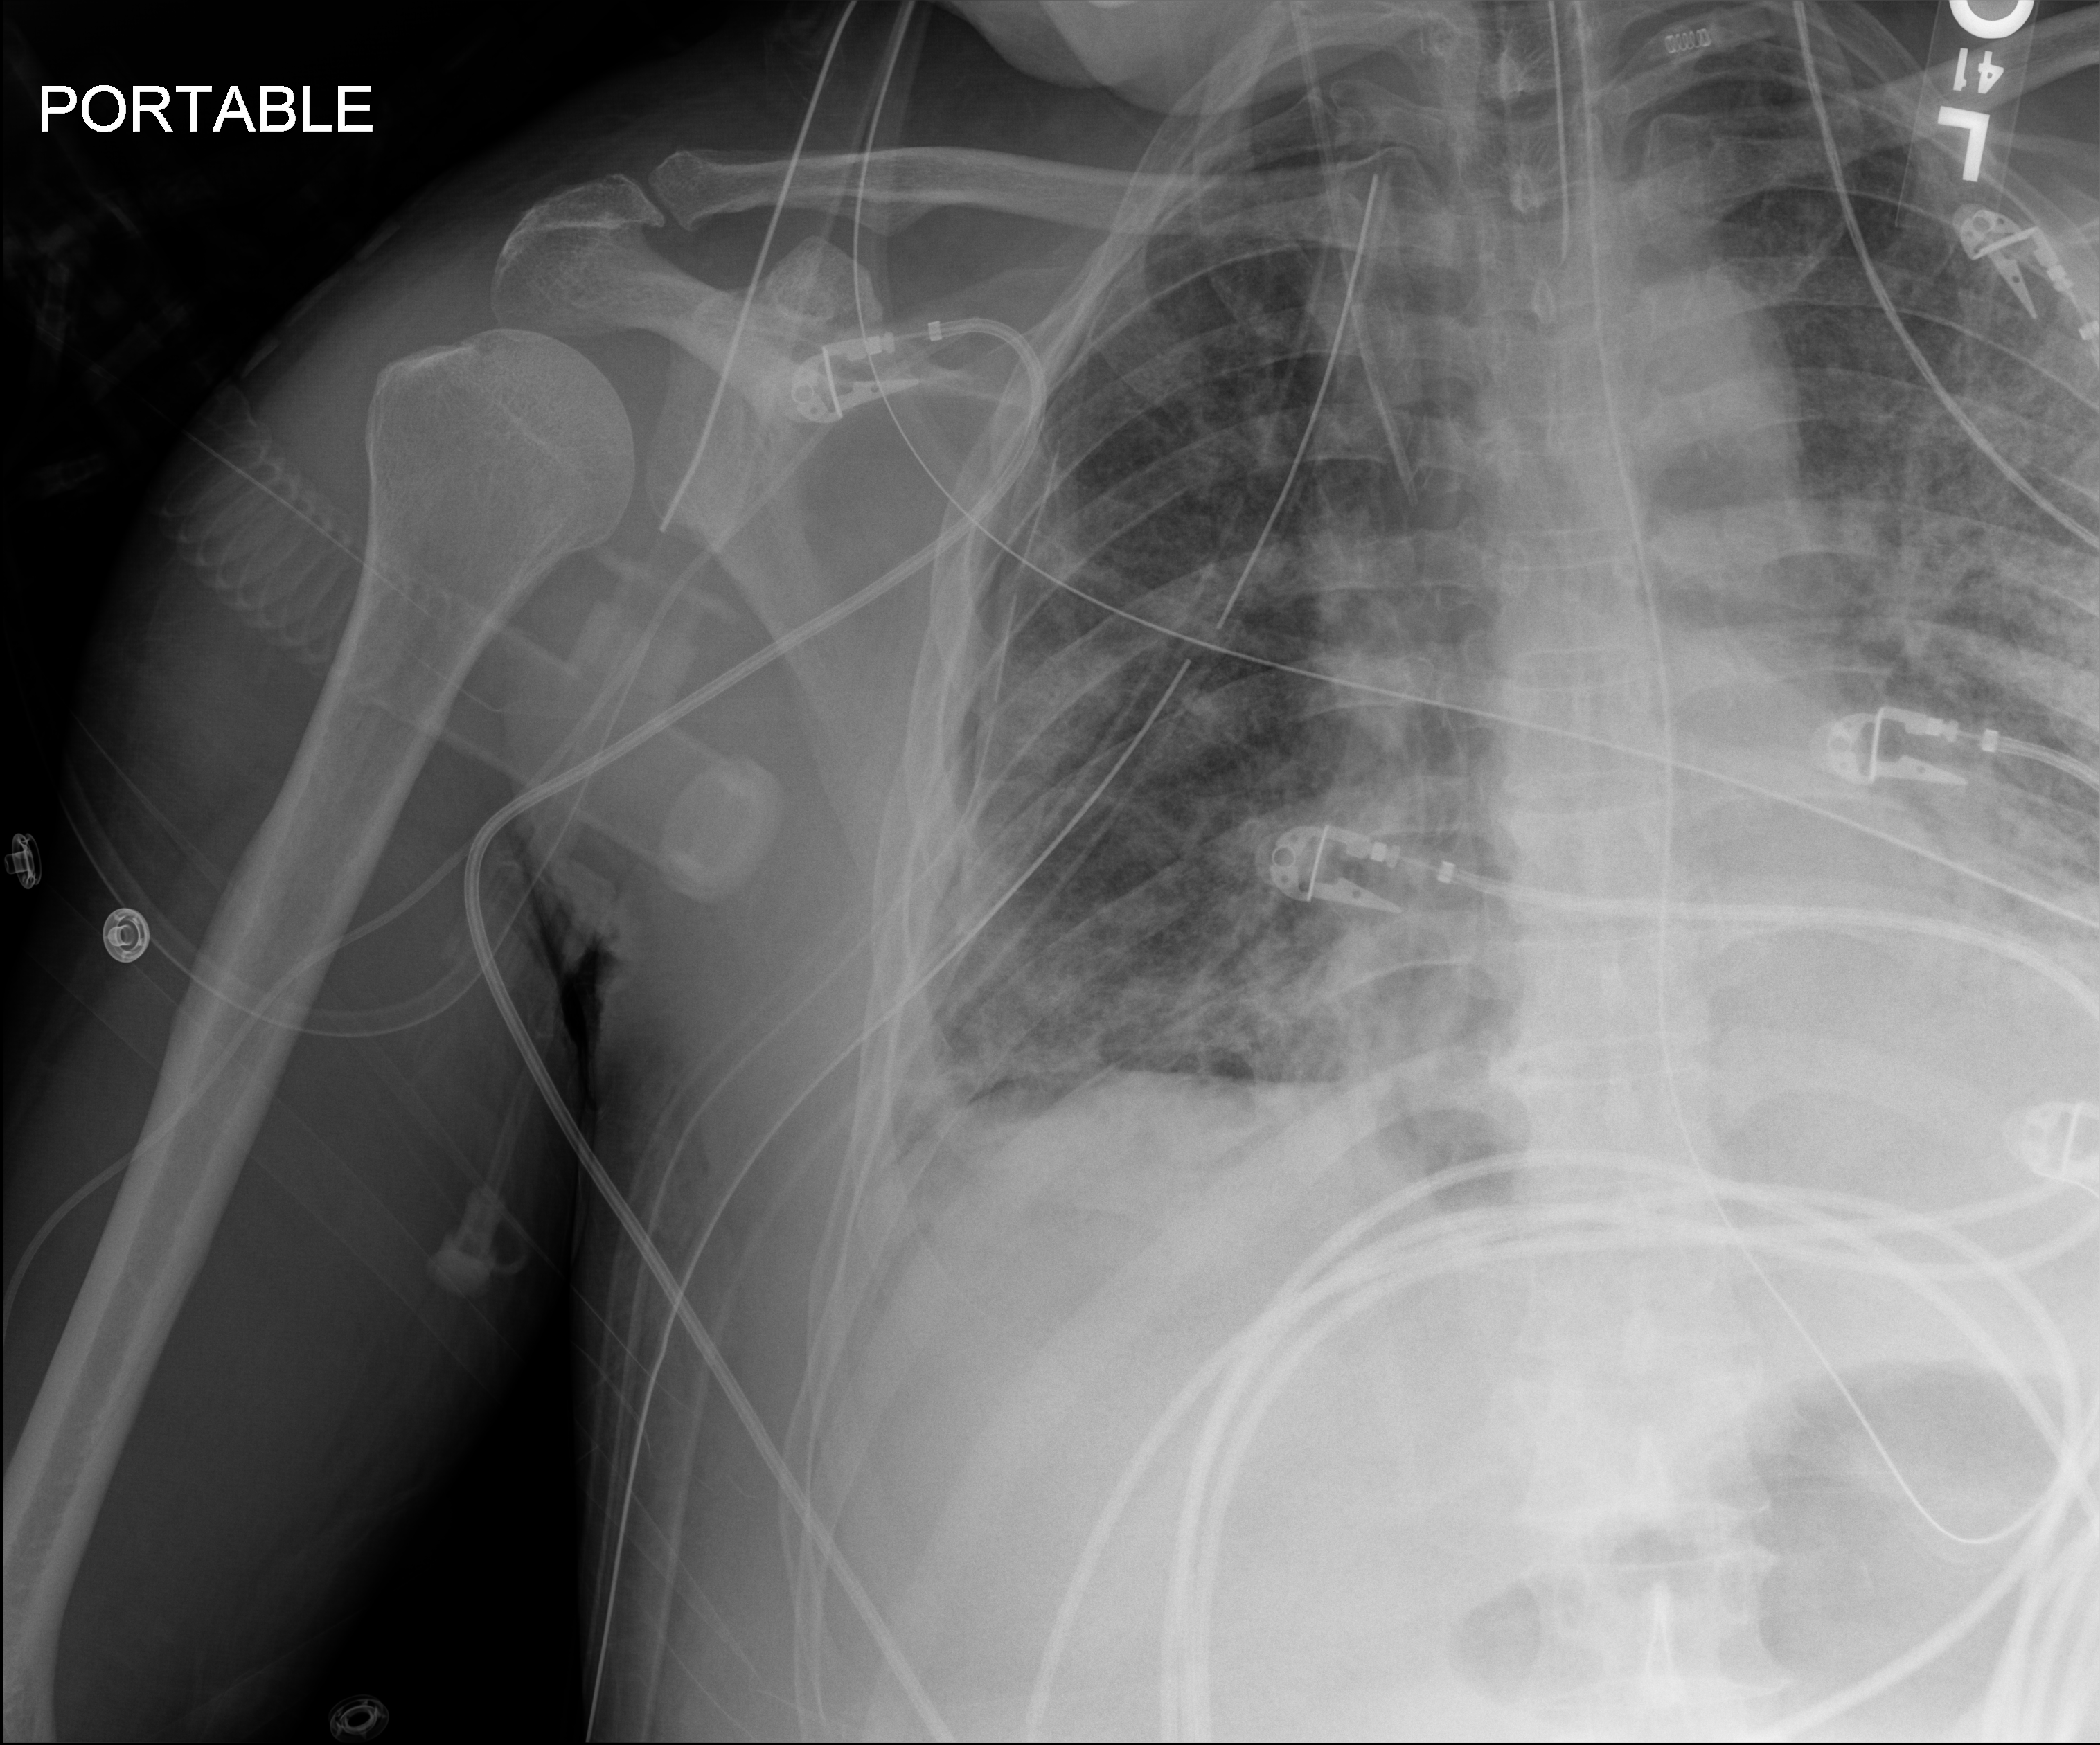
Bedside chest radiograph (digital radiography); anteroposterior (AP) projection. Male patient hospitalised with COVID-19, age 60–74 years.
Admission-level facts for this patient (not findings on this image; timing relative to this image not recorded): mechanically ventilated during this hospital stay: yes; diabetes (admission record): yes; hypertension (admission record): yes.